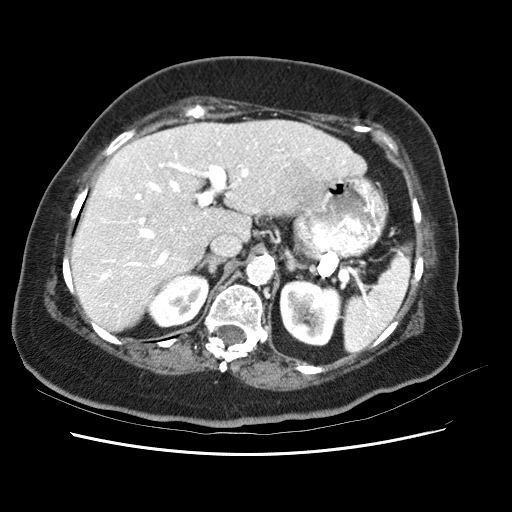
Contrast-enhanced abdominal CT (liver protocol), one axial slice; slice 40 of 62 in the series (ordered by position); 120 kVp; soft-tissue window (W 400 / L 40 HU); 2.5 mm slice thickness; 512 × 512 image matrix. Case-level facts recorded for this patient, not image findings: diagnosis: hepatocellular carcinoma (patient treated with transarterial chemoembolisation; whether this scan precedes or follows treatment is not stated here); TNM stage (as recorded): Stage-I; Child-Pugh class: B; tumour nodularity: uninodular; tumour size: 5.3 cm.
Outlined on this slice (semi-automatic segmentation, software-assisted and operator-edited):
- liver parenchyma outside the tumour (the mass and vessels are separate outlines, so this box may not span the whole liver): bounding box [x1, y1, x2, y2] px = [72, 119, 362, 330]
- mass: [263, 148, 322, 218]
- liver vessels: [86, 129, 332, 302]